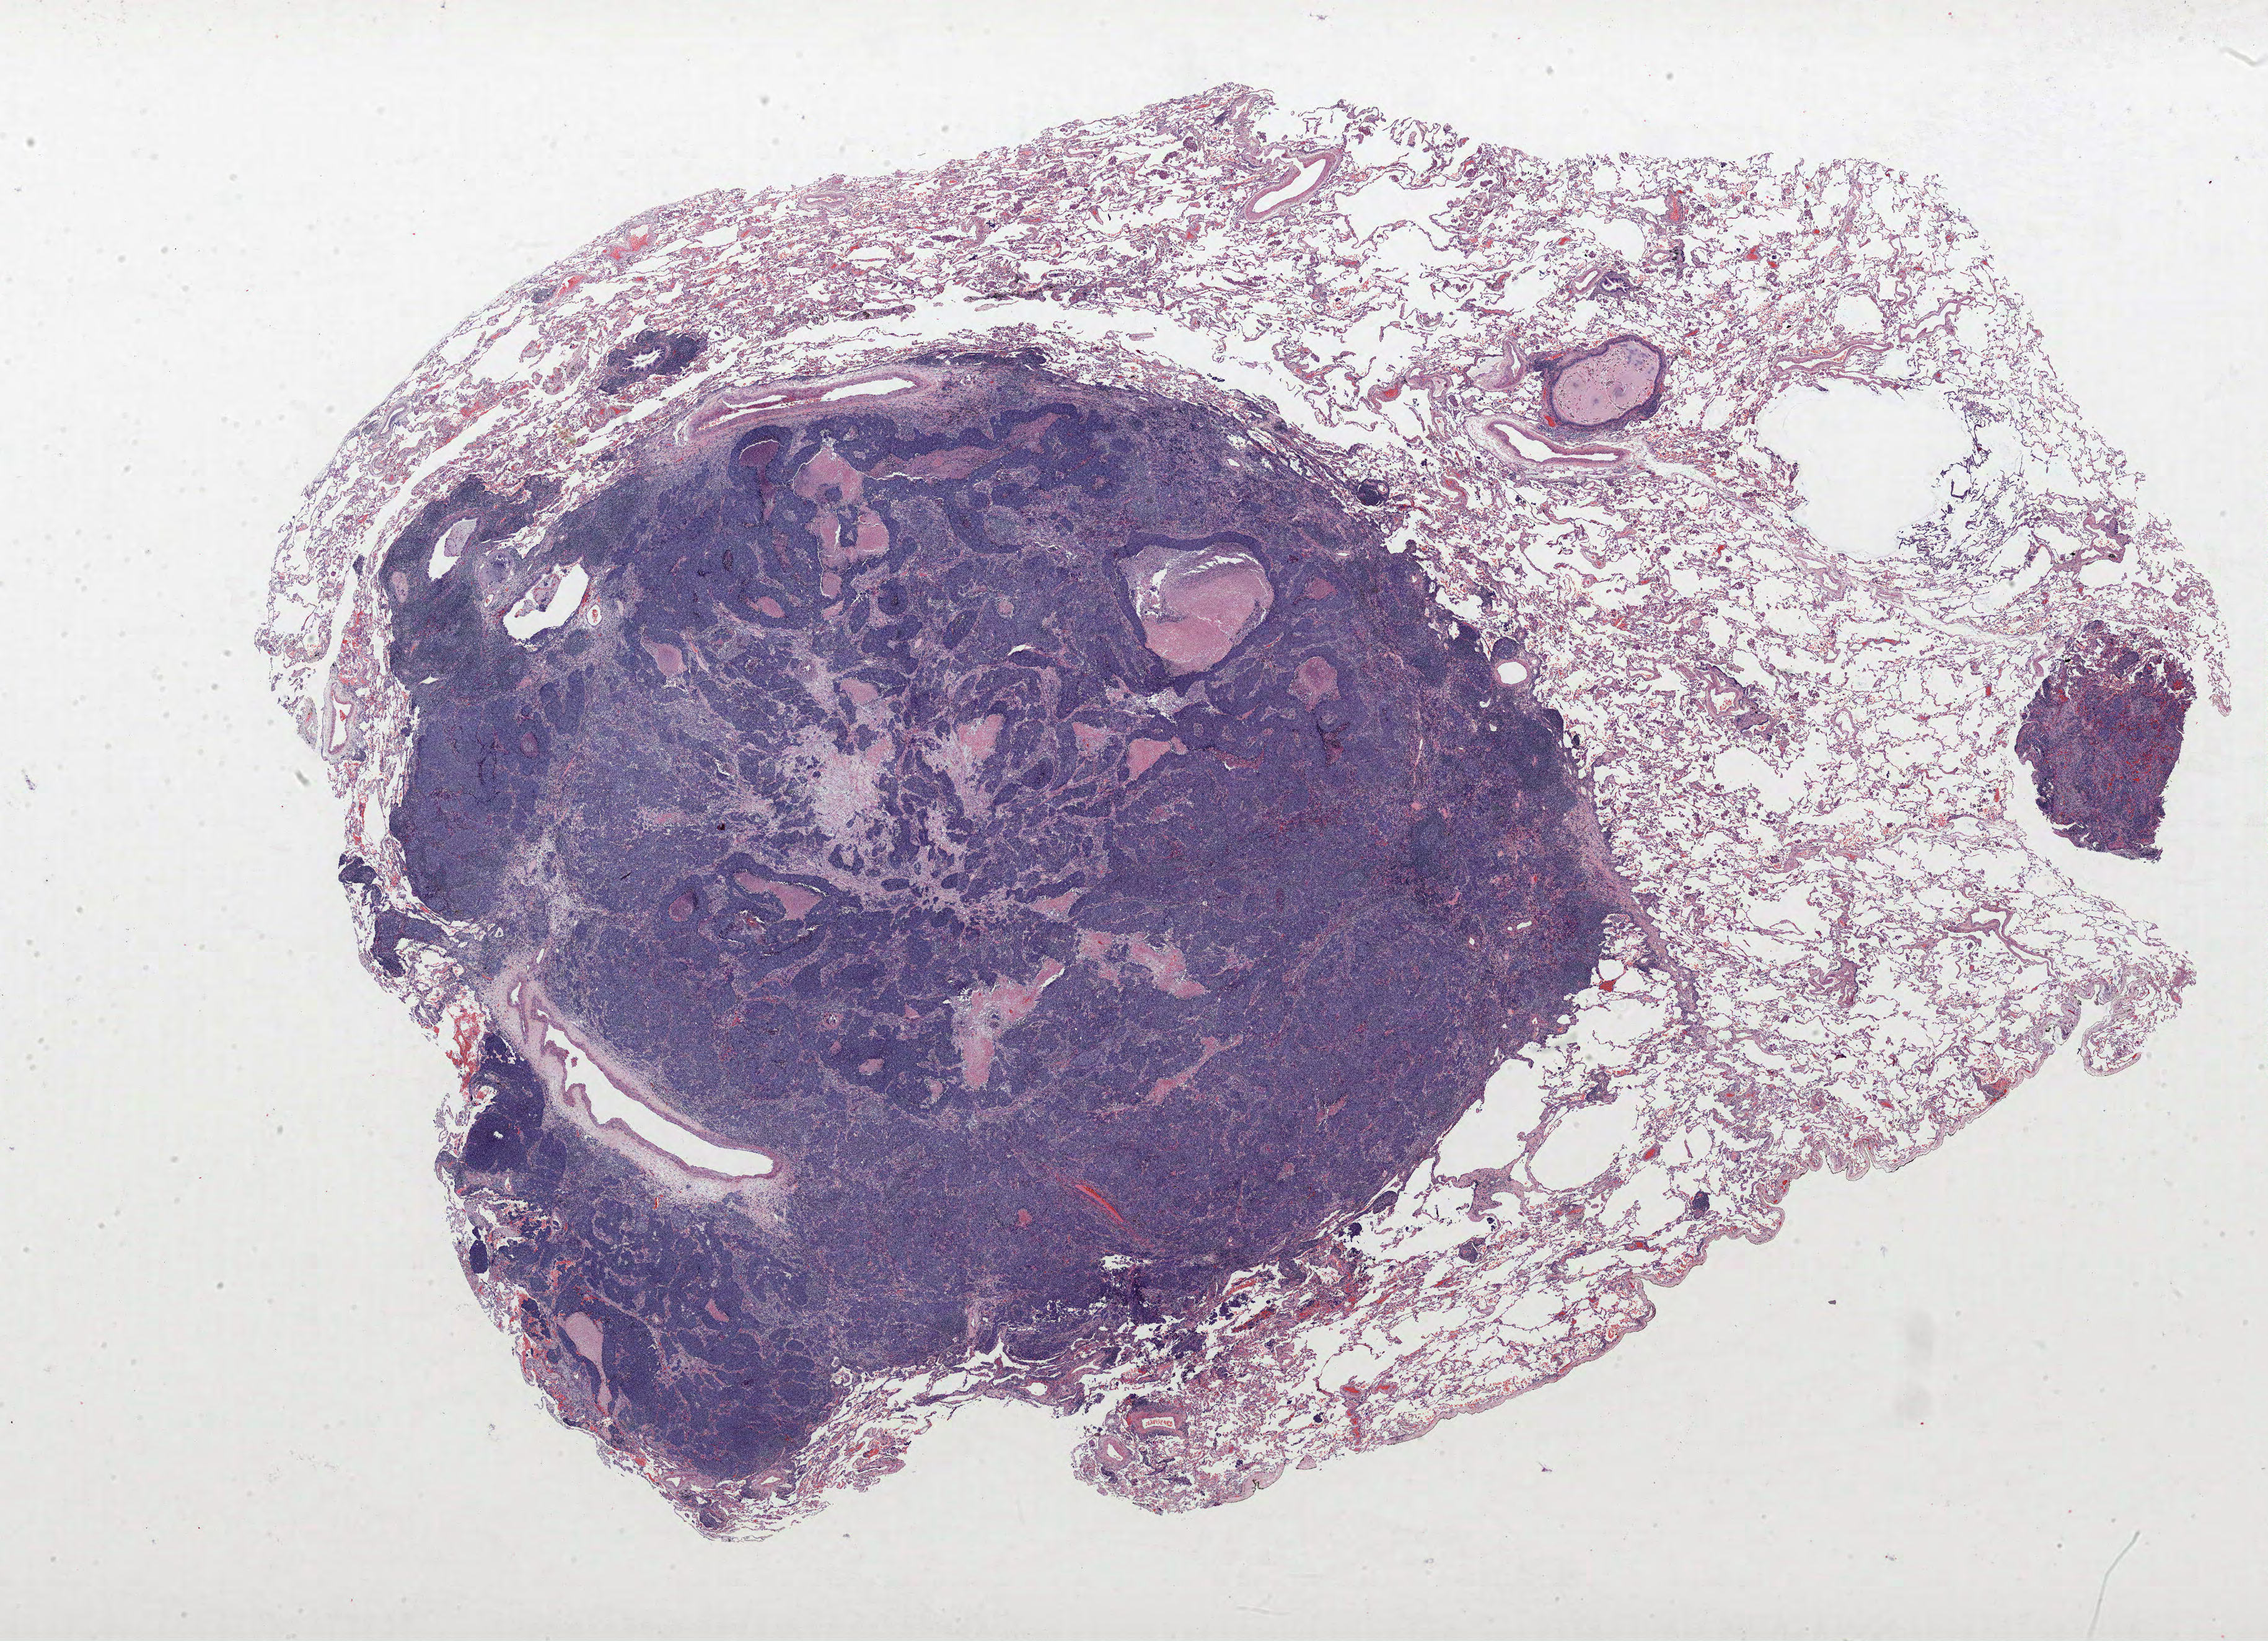
Whole-slide histology image, H&E-stained — low-resolution overview of the scanned area, about 29.3 x 21.2 mm (slide scanned at 40x). FFPE section. Lung tissue. Female patient, aged 55 at enrolment.
Tumour size (pathology): 24 mm. ICD-O-3 topography: middle lobe of lung (C34.2). Stage (AJCC 6th edition): IIB. Primary tumour location (clinical record): right middle lobe. Participant's lung-cancer diagnosis: Small cell carcinoma, NOS (ICD-O-3 8041/3).